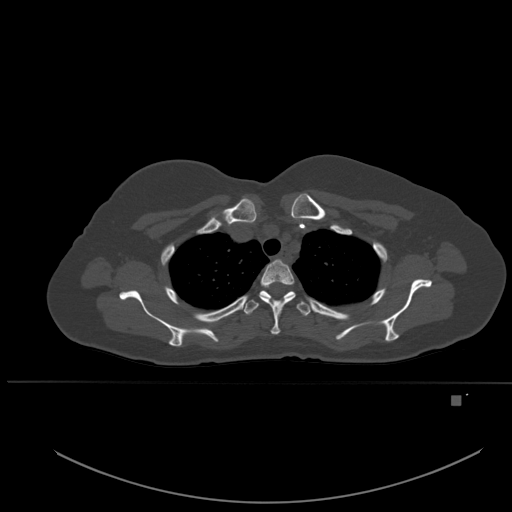
CT including the spine, one axial slice. Position 401 of 651 along the scan axis. Bone window (W 1800 / L 400 HU). 1.5 mm slice thickness. 512 × 512 image matrix, field of view 443 × 443 mm. Patient: female, 49 years. From the clinical record (not read from this slice): primary cancer: breast.
Outlined on this slice (semi-automatically segmented with operator editing):
- T2 vertebra: bounding box [x1, y1, x2, y2] px = [260, 259, 296, 335]
- T3 vertebra: [244, 290, 313, 316]